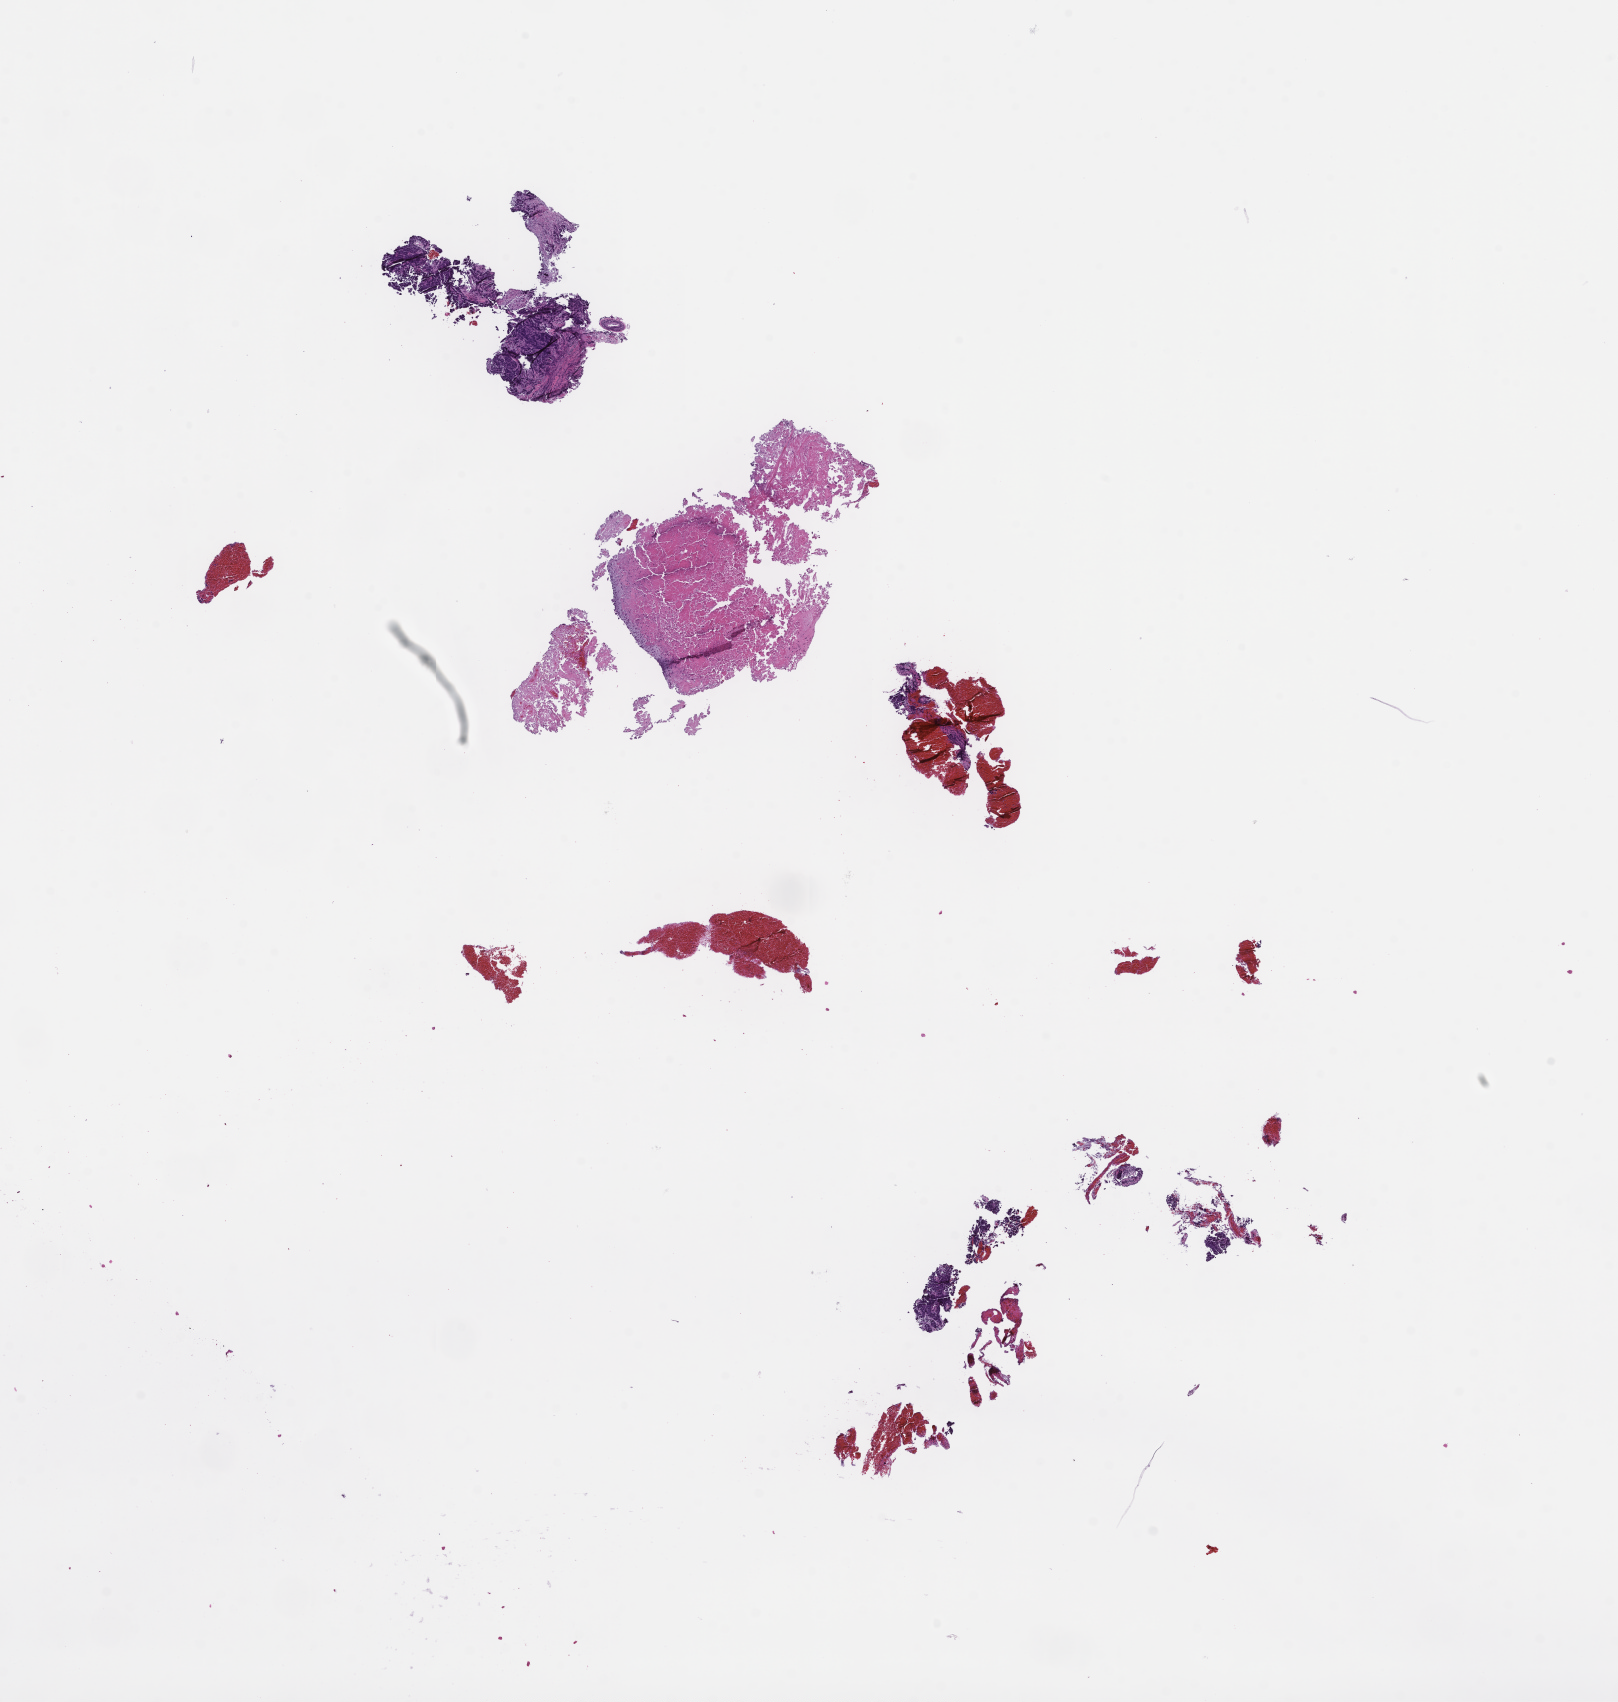
Haematoxylin and eosin whole-slide image, whole scanned area (about 13.1 x 13.7 mm) shown as a low-resolution overview. FFPE section. Tissue site: lung. Specimen time point: archival tissue. Patient sex: male.
This section: primary tumor. Diagnosis: Non-Small Cell Lung Carcinoma.